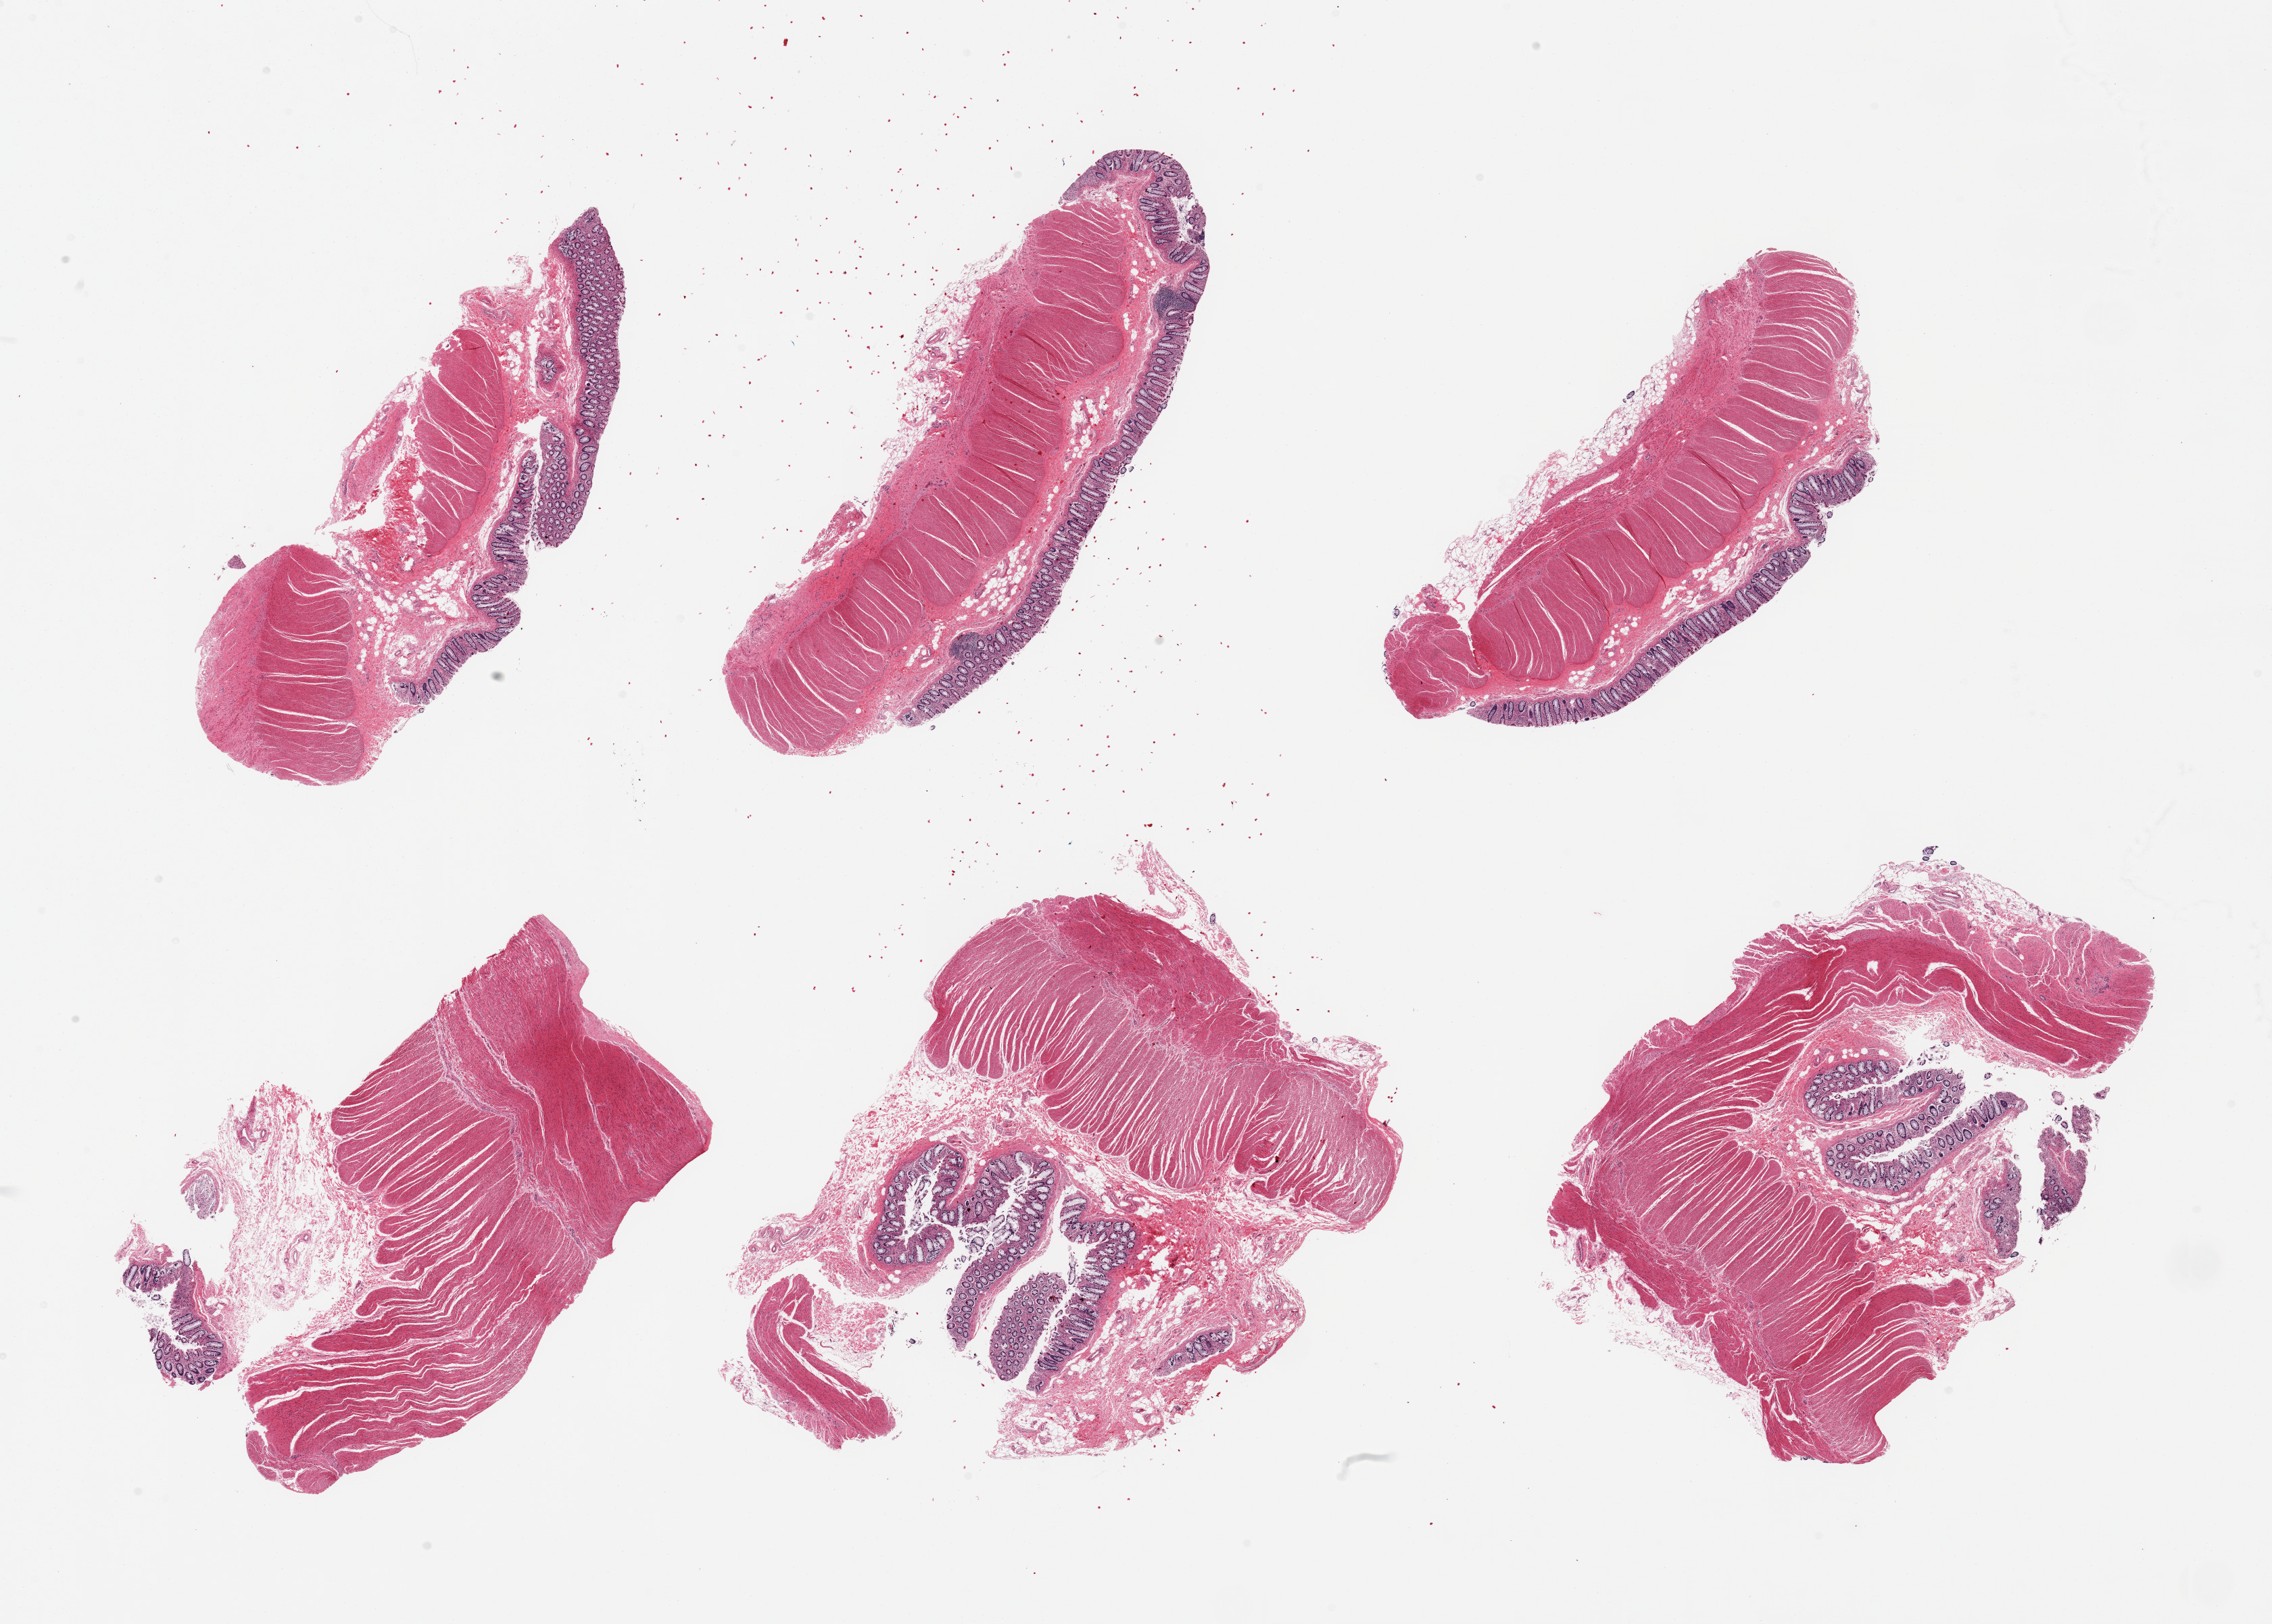
Whole-slide image, hematoxylin and eosin (H&E) stain, brightfield, low-resolution overview of the scanned area, about 26.6 x 19.0 mm. Donor: female.
* specimen: PAXgene-fixed paraffin-embedded (PFPE) section; target tissue: sigmoid colon; donor tissue sample